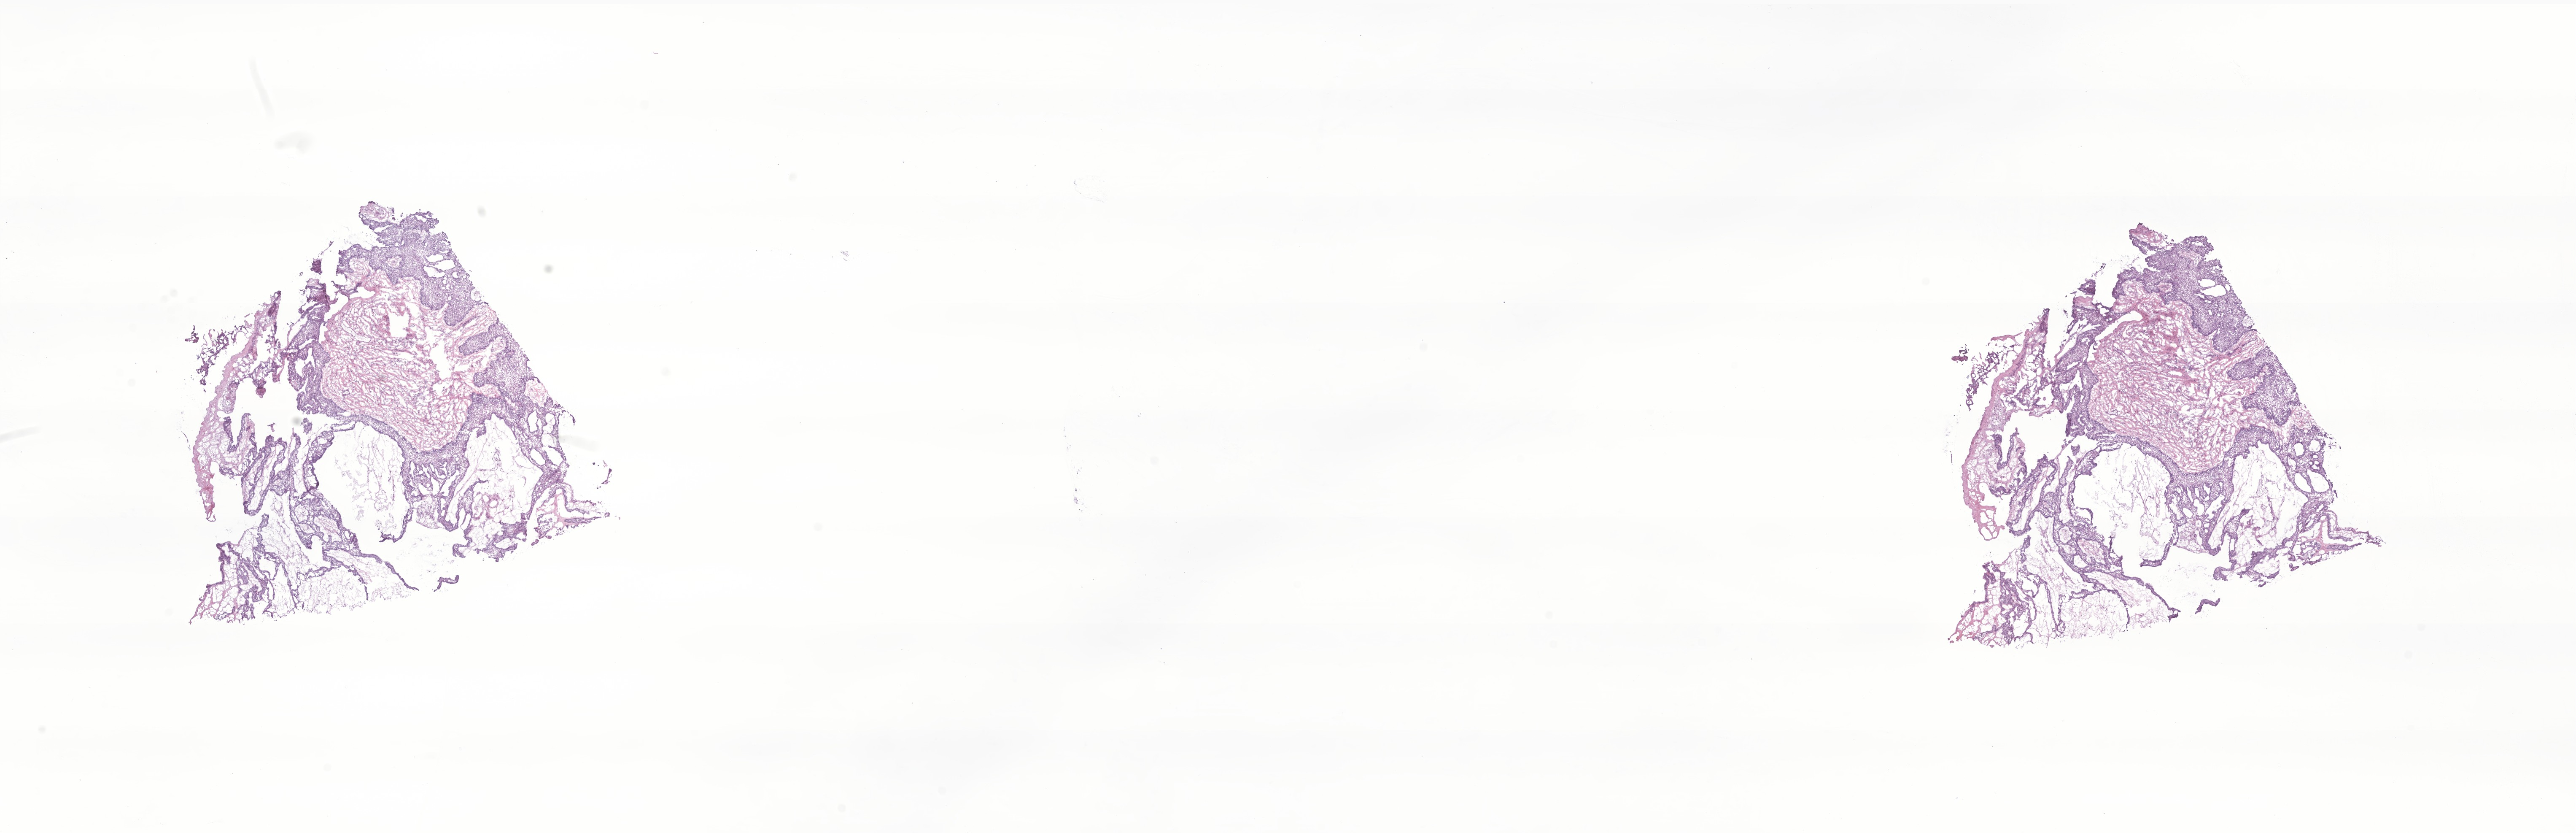
Digitized hematoxylin and eosin (H&E)-stained section of tumor tissue from the brain, a low-resolution overview of the entire scanned area, about 25.8 x 8.3 mm, cryosection (OCT / tissue freezing medium). Patient female; age 70 months (5 years 10 months).
Diagnosis: Craniopharyngioma, adamantinomatous.